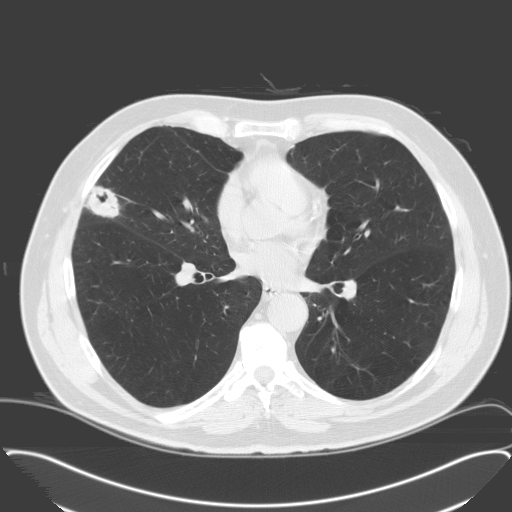
Low-dose screening chest CT, axial slice. Third annual screen. Lung window (W 1500 / L -600 HU). Standard (soft-tissue) reconstruction kernel (C). Slice 88 of 174 in the series. Male, age 65 years at enrolment. Former smoker at enrolment.
• Expert reader's lesion annotation, box from (x=68, y=175) to (x=131, y=231) px.
• The exam's reader record, not a measurement of the box and not confirmed to be the same lesion: non-calcified nodule or mass ≥4 mm, right middle lobe, 28 × 23 mm, spiculated (stellate) margins, soft tissue attenuation, pre-existing on the prior screen: no.
• Official screen result: positive, other.
• Participant outcome: lung cancer diagnosed 25 days after this screen — adenocarcinoma, NOS, right middle lobe, moderately differentiated (G2), stage IA (AJCC 6th edition), 25 mm at pathology.